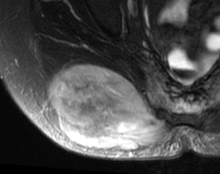
MRI of an extremity soft-tissue mass, one axial slice; position 29 of 63 along the scan axis; T2-weighted fat-saturated; MR volume resampled by the dataset authors to the PET/CT grid (not the native acquisition matrix); 3.27 mm slice thickness; 220 × 174 image matrix, field of view 215 × 170 mm. Female patient. From the clinical record (not read from this slice): histological type: spindle cell suggestive of myxofibrosarcoma; grade: intermediate; site of the primary tumour: right buttock.
Structures marked on this image (expert contour drawn on MRI and transferred to this co-registered scan by the dataset authors):
- gross tumour volume (mass): bounding box (x1, y1, x2, y2) in pixels: (50, 64, 174, 151)